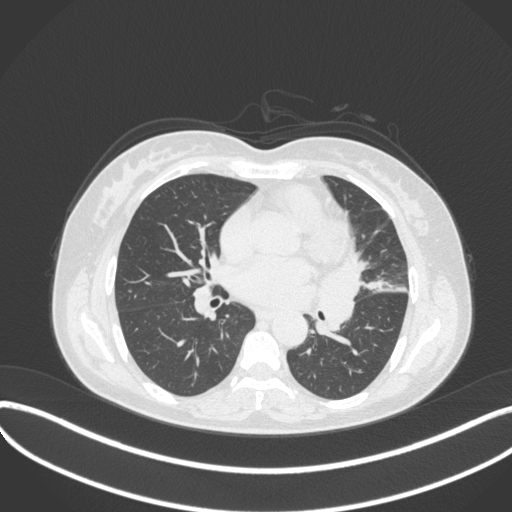
Chest CT, one axial slice; position 175 of 373 along the scan axis; reconstruction kernel B31f; 120 kVp; lung window (W 1500 / L -600 HU); 1 mm slice thickness; 512 × 512 image matrix. Patient: female, 54 years. Case-level facts recorded for this patient, not image findings: clinical TNM (as recorded): T2a N1 M0.
Outlined on this slice (rectangle marked by the reading radiologist):
- lung tumour (recorded histology: small cell carcinoma): bounding box [x1, y1, x2, y2] px = [311, 257, 373, 348]